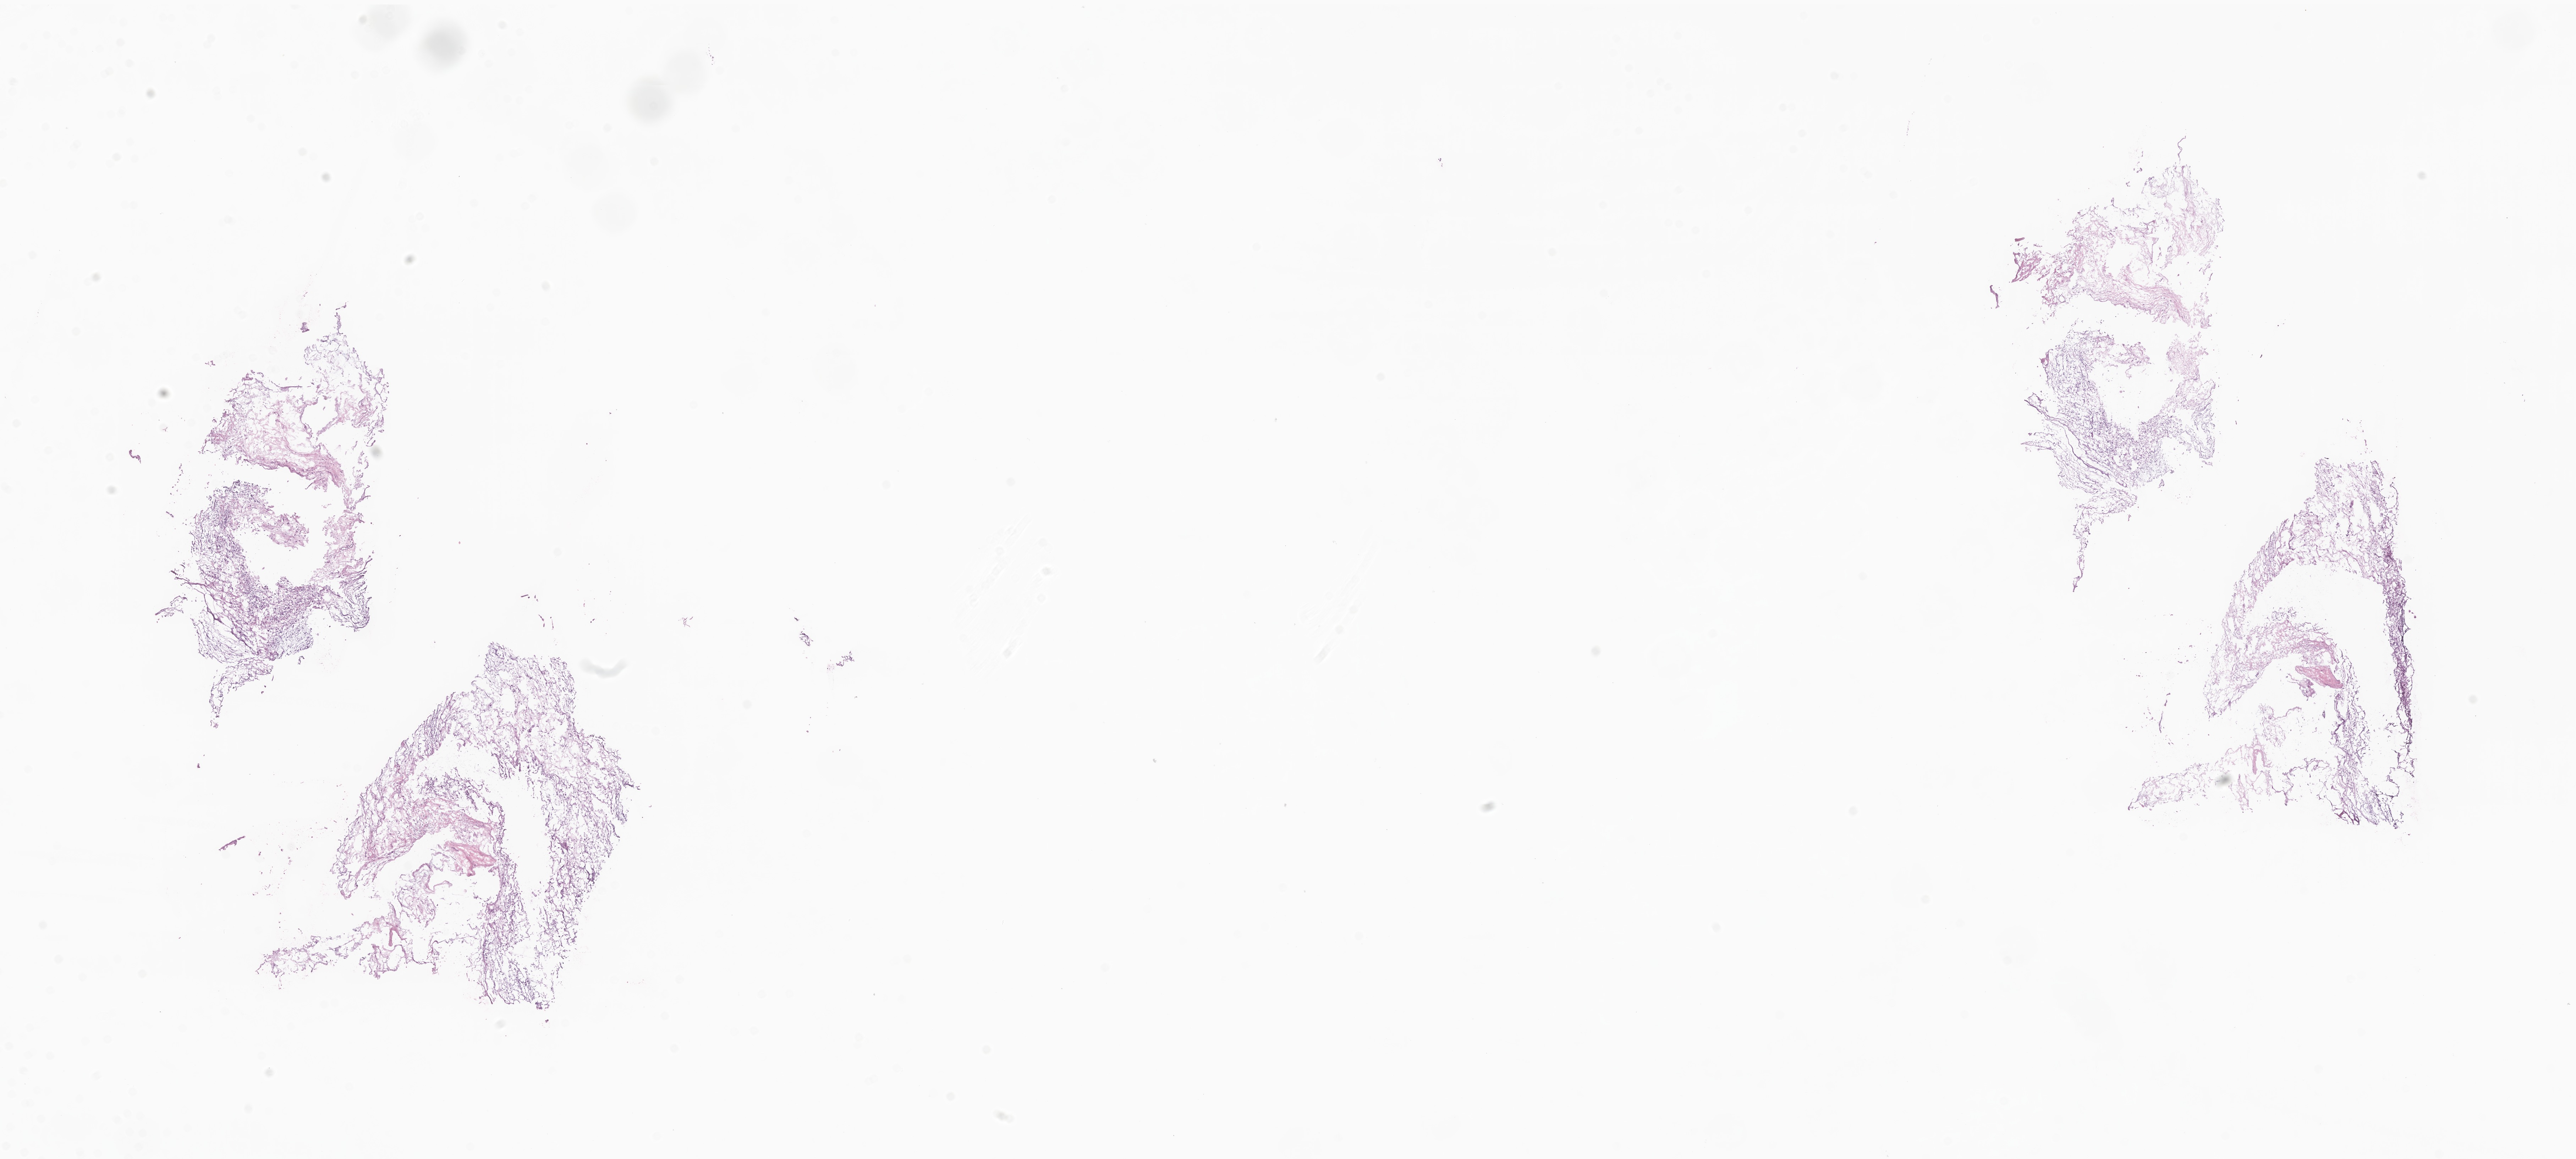
H&E whole-slide image of tumor tissue from the liver — whole scanned area (about 30.6 x 13.8 mm) shown as a low-resolution overview; frozen section. Female patient, age 145 months (12 years 1 month).
Diagnosis (ICD-O-3 morphology term): Embryonal sarcoma.